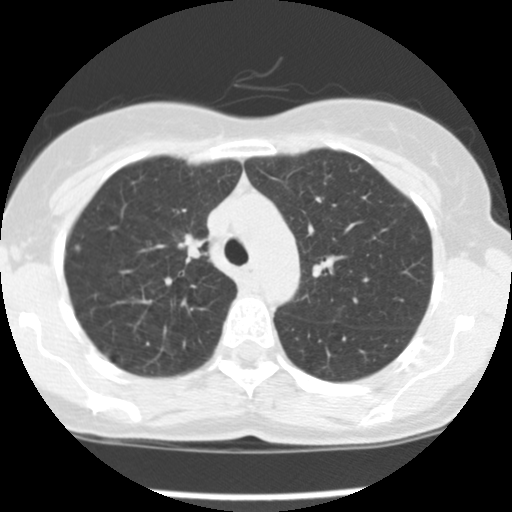
Low-dose screening chest CT, axial slice, first (baseline) screen, lung window (W 1500 / L -600 HU), 2.5 mm slice thickness, standard (soft-tissue) reconstruction kernel (STANDARD), 120 kVp, slice 113 of 157 in the series. Female, age 57 years at enrolment.
Expert-annotated lung lesion, bounding box <166,226,217,270> (left, top, right, bottom; pixels). Screening reader's record for this exam (one nodule recorded; not confirmed to be the boxed lesion): non-calcified nodule or mass ≥4 mm, left upper lobe, 7 × 6 mm, poorly defined margins, ground glass attenuation. Note: the box lies in the patient's right hemithorax on this image, whereas the reader's record names the left lung; they may be different findings. Official screen result: positive, change unspecified: nodule(s) >= 4 mm or enlarging nodule(s), mass(es), or other non-specific abnormalities suspicious for lung cancer.